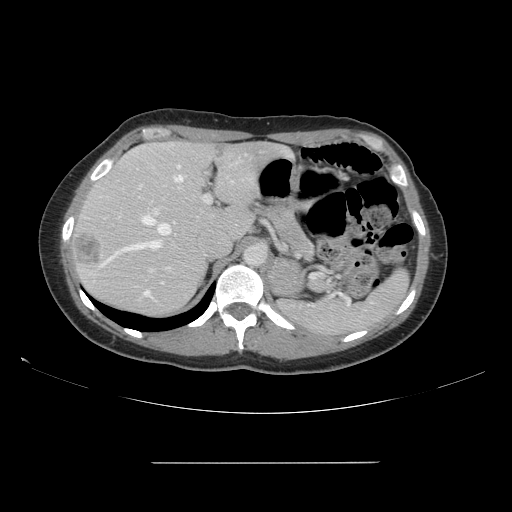
Contrast-enhanced abdominal CT, one axial slice. Position 108 of 151 along the scan axis. Soft-tissue window (W 400 / L 40 HU). 2.5 mm slice thickness. 512 × 512 image matrix, field of view 421 × 421 mm. Female patient, age 46 years. From the clinical record (not read from this slice): diagnosis: colorectal cancer liver metastases, imaged before liver resection; multiple liver metastases: yes; largest metastasis: 3 cm; disease in both lobes: yes.
Structures marked on this image (expert manual segmentation):
- hepatic veins: bounding box (x1, y1, x2, y2) in pixels: (99, 161, 239, 267)
- liver: (71, 142, 283, 317)
- planned liver remnant (the part of the liver to remain after resection): (88, 142, 284, 252)
- portal vein (with intrahepatic branches): (139, 184, 211, 296)
- liver metastasis: (73, 235, 102, 267)
- liver metastasis: (216, 145, 225, 157)